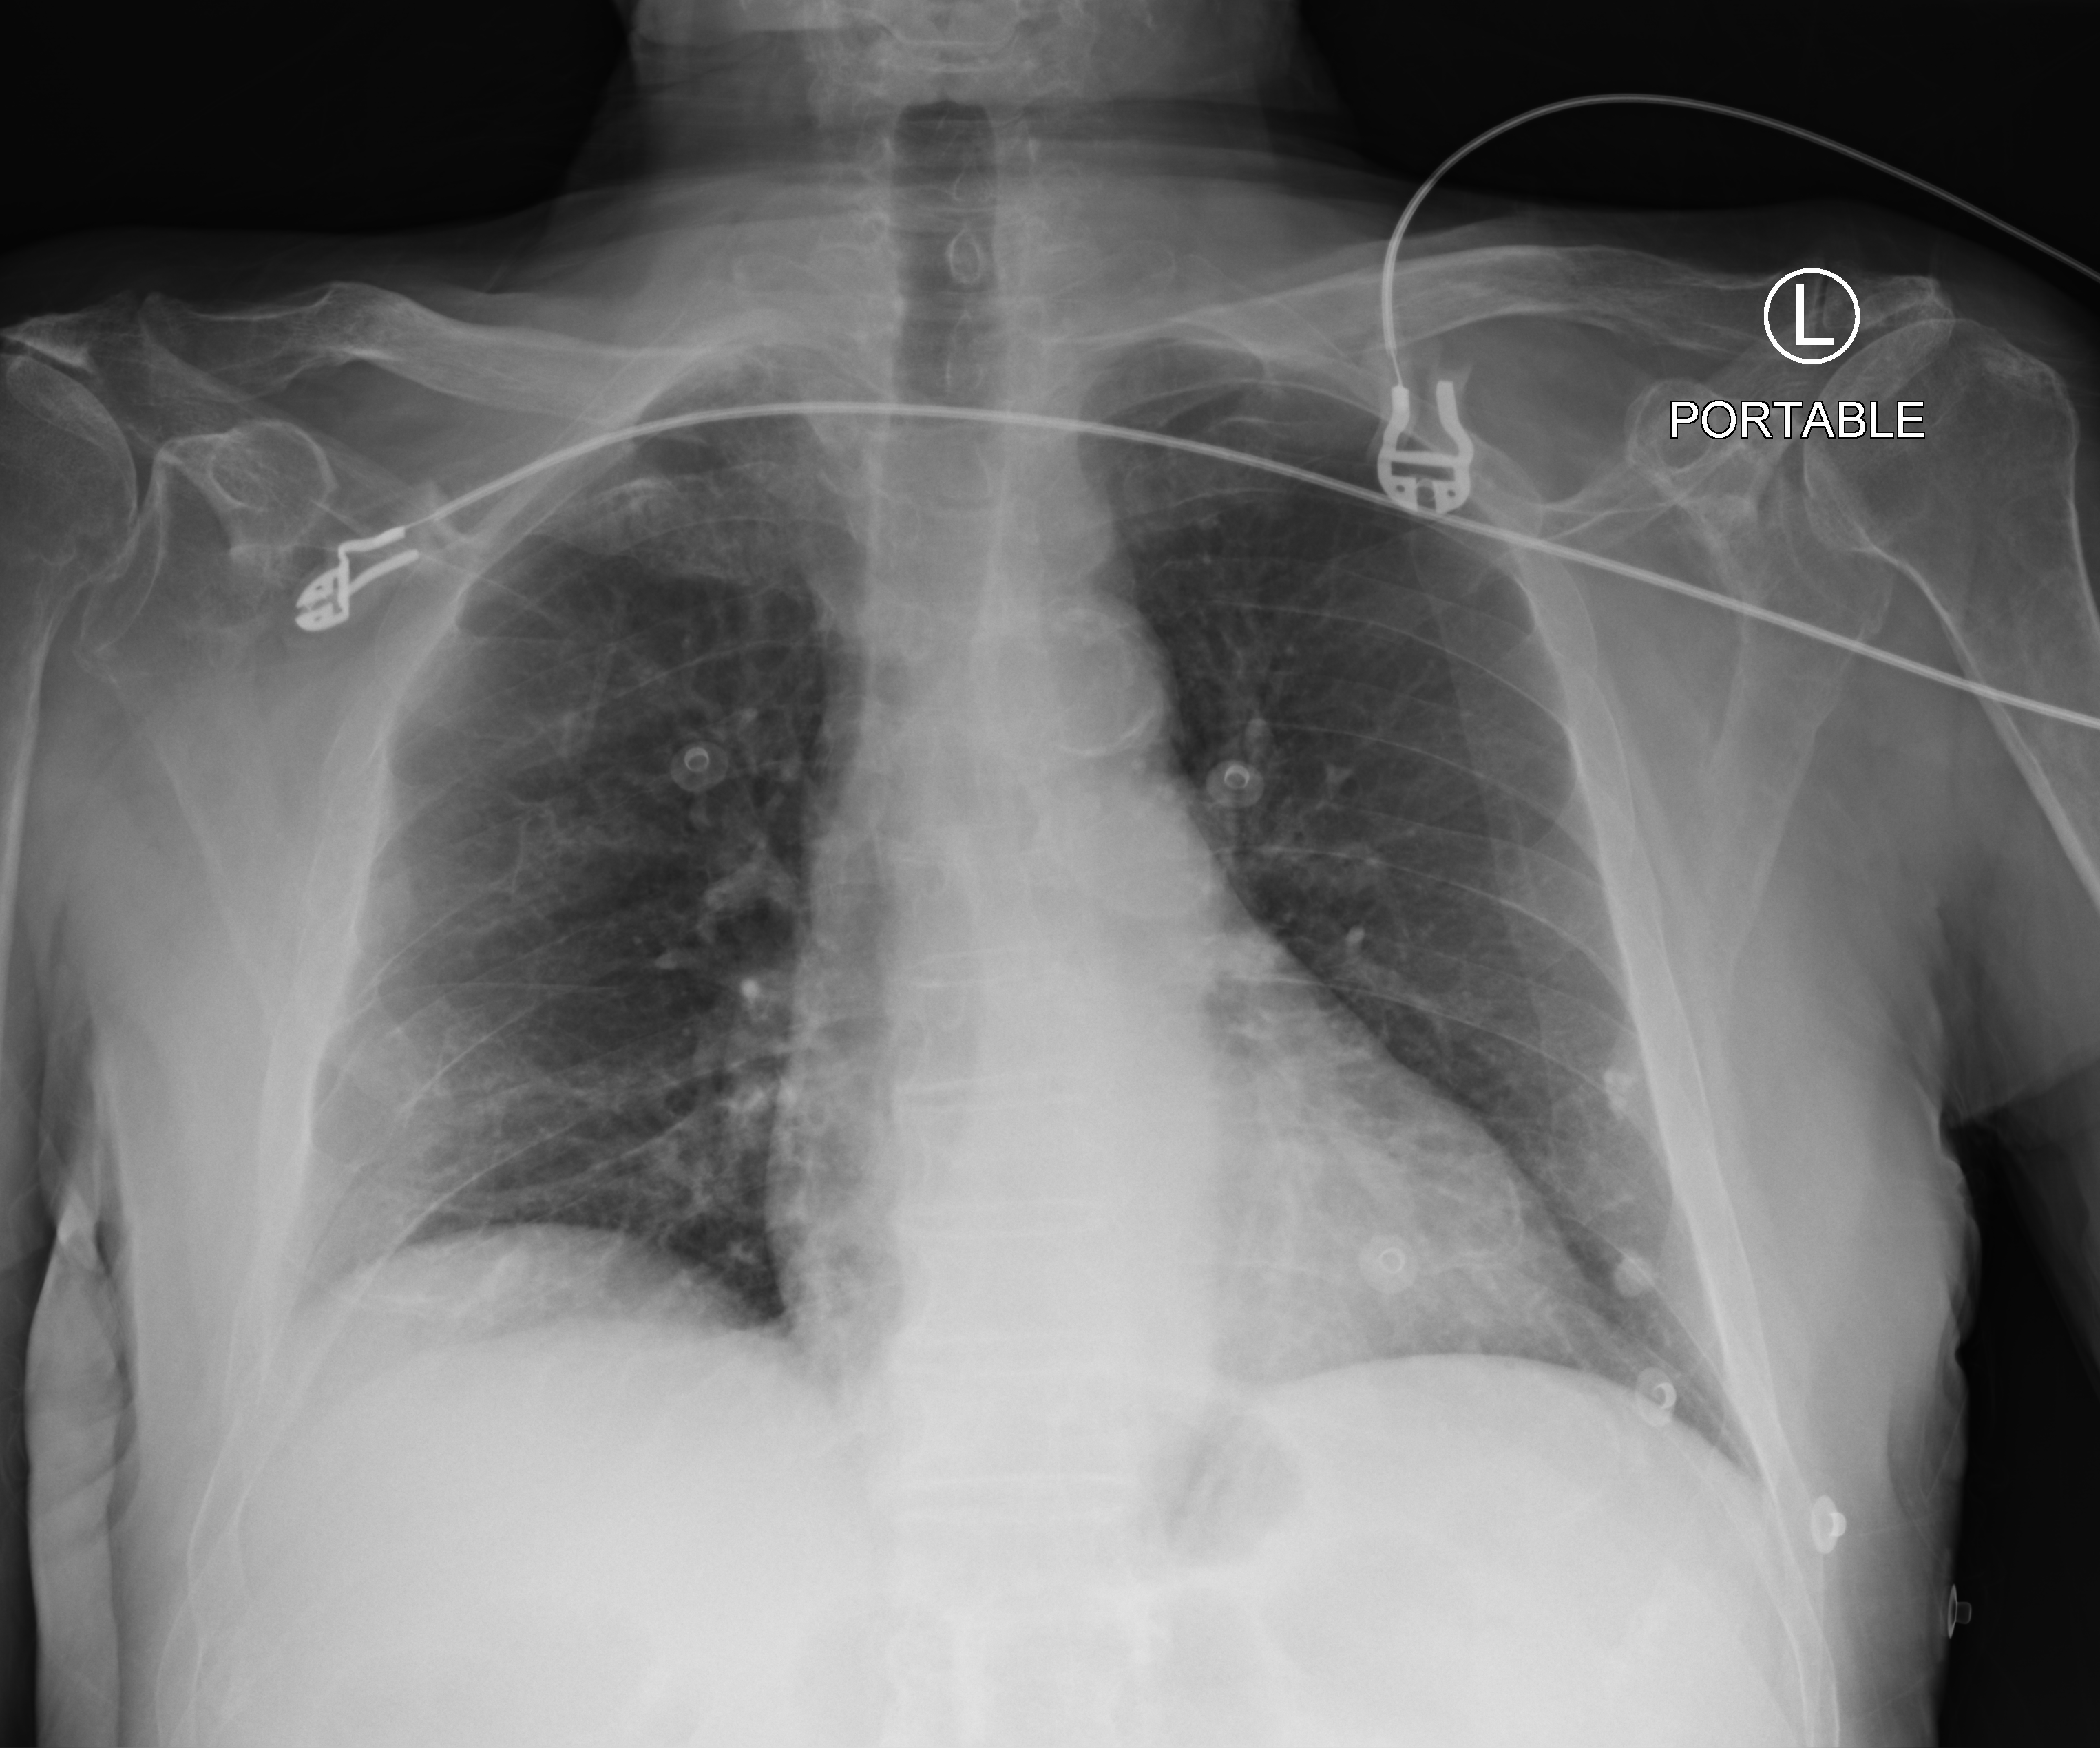
Chest X-ray (portable). Male patient hospitalised with COVID-19, age 75–90 years.
Admission-level facts for this patient (not findings on this image; timing relative to this image not recorded): length of hospital stay: 9 days.